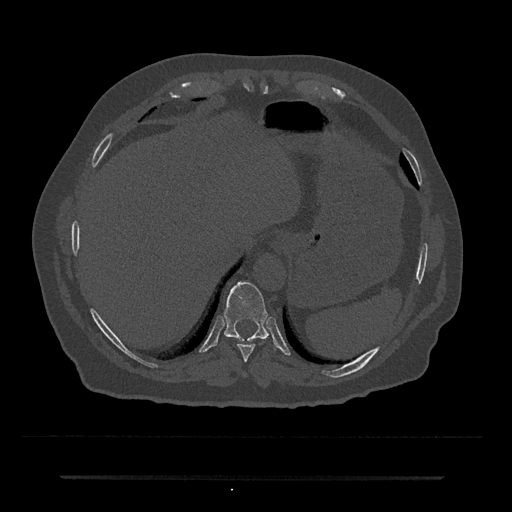
CT including the spine, one axial slice; position 248 of 797 along the scan axis; 120 kVp; bone window (W 1800 / L 400 HU); 0.5 mm slice thickness; 512 × 512 image matrix, field of view 437 × 437 mm. Patient: male, 69 years. From the clinical record (not read from this slice): primary cancer: prostate.
Structures marked on this image (semi-automatic segmentation, software-assisted and operator-edited):
- T10 vertebra: bounding box (x1, y1, x2, y2) in pixels: (224, 282, 268, 342)
- T9 vertebra: (237, 344, 256, 362)